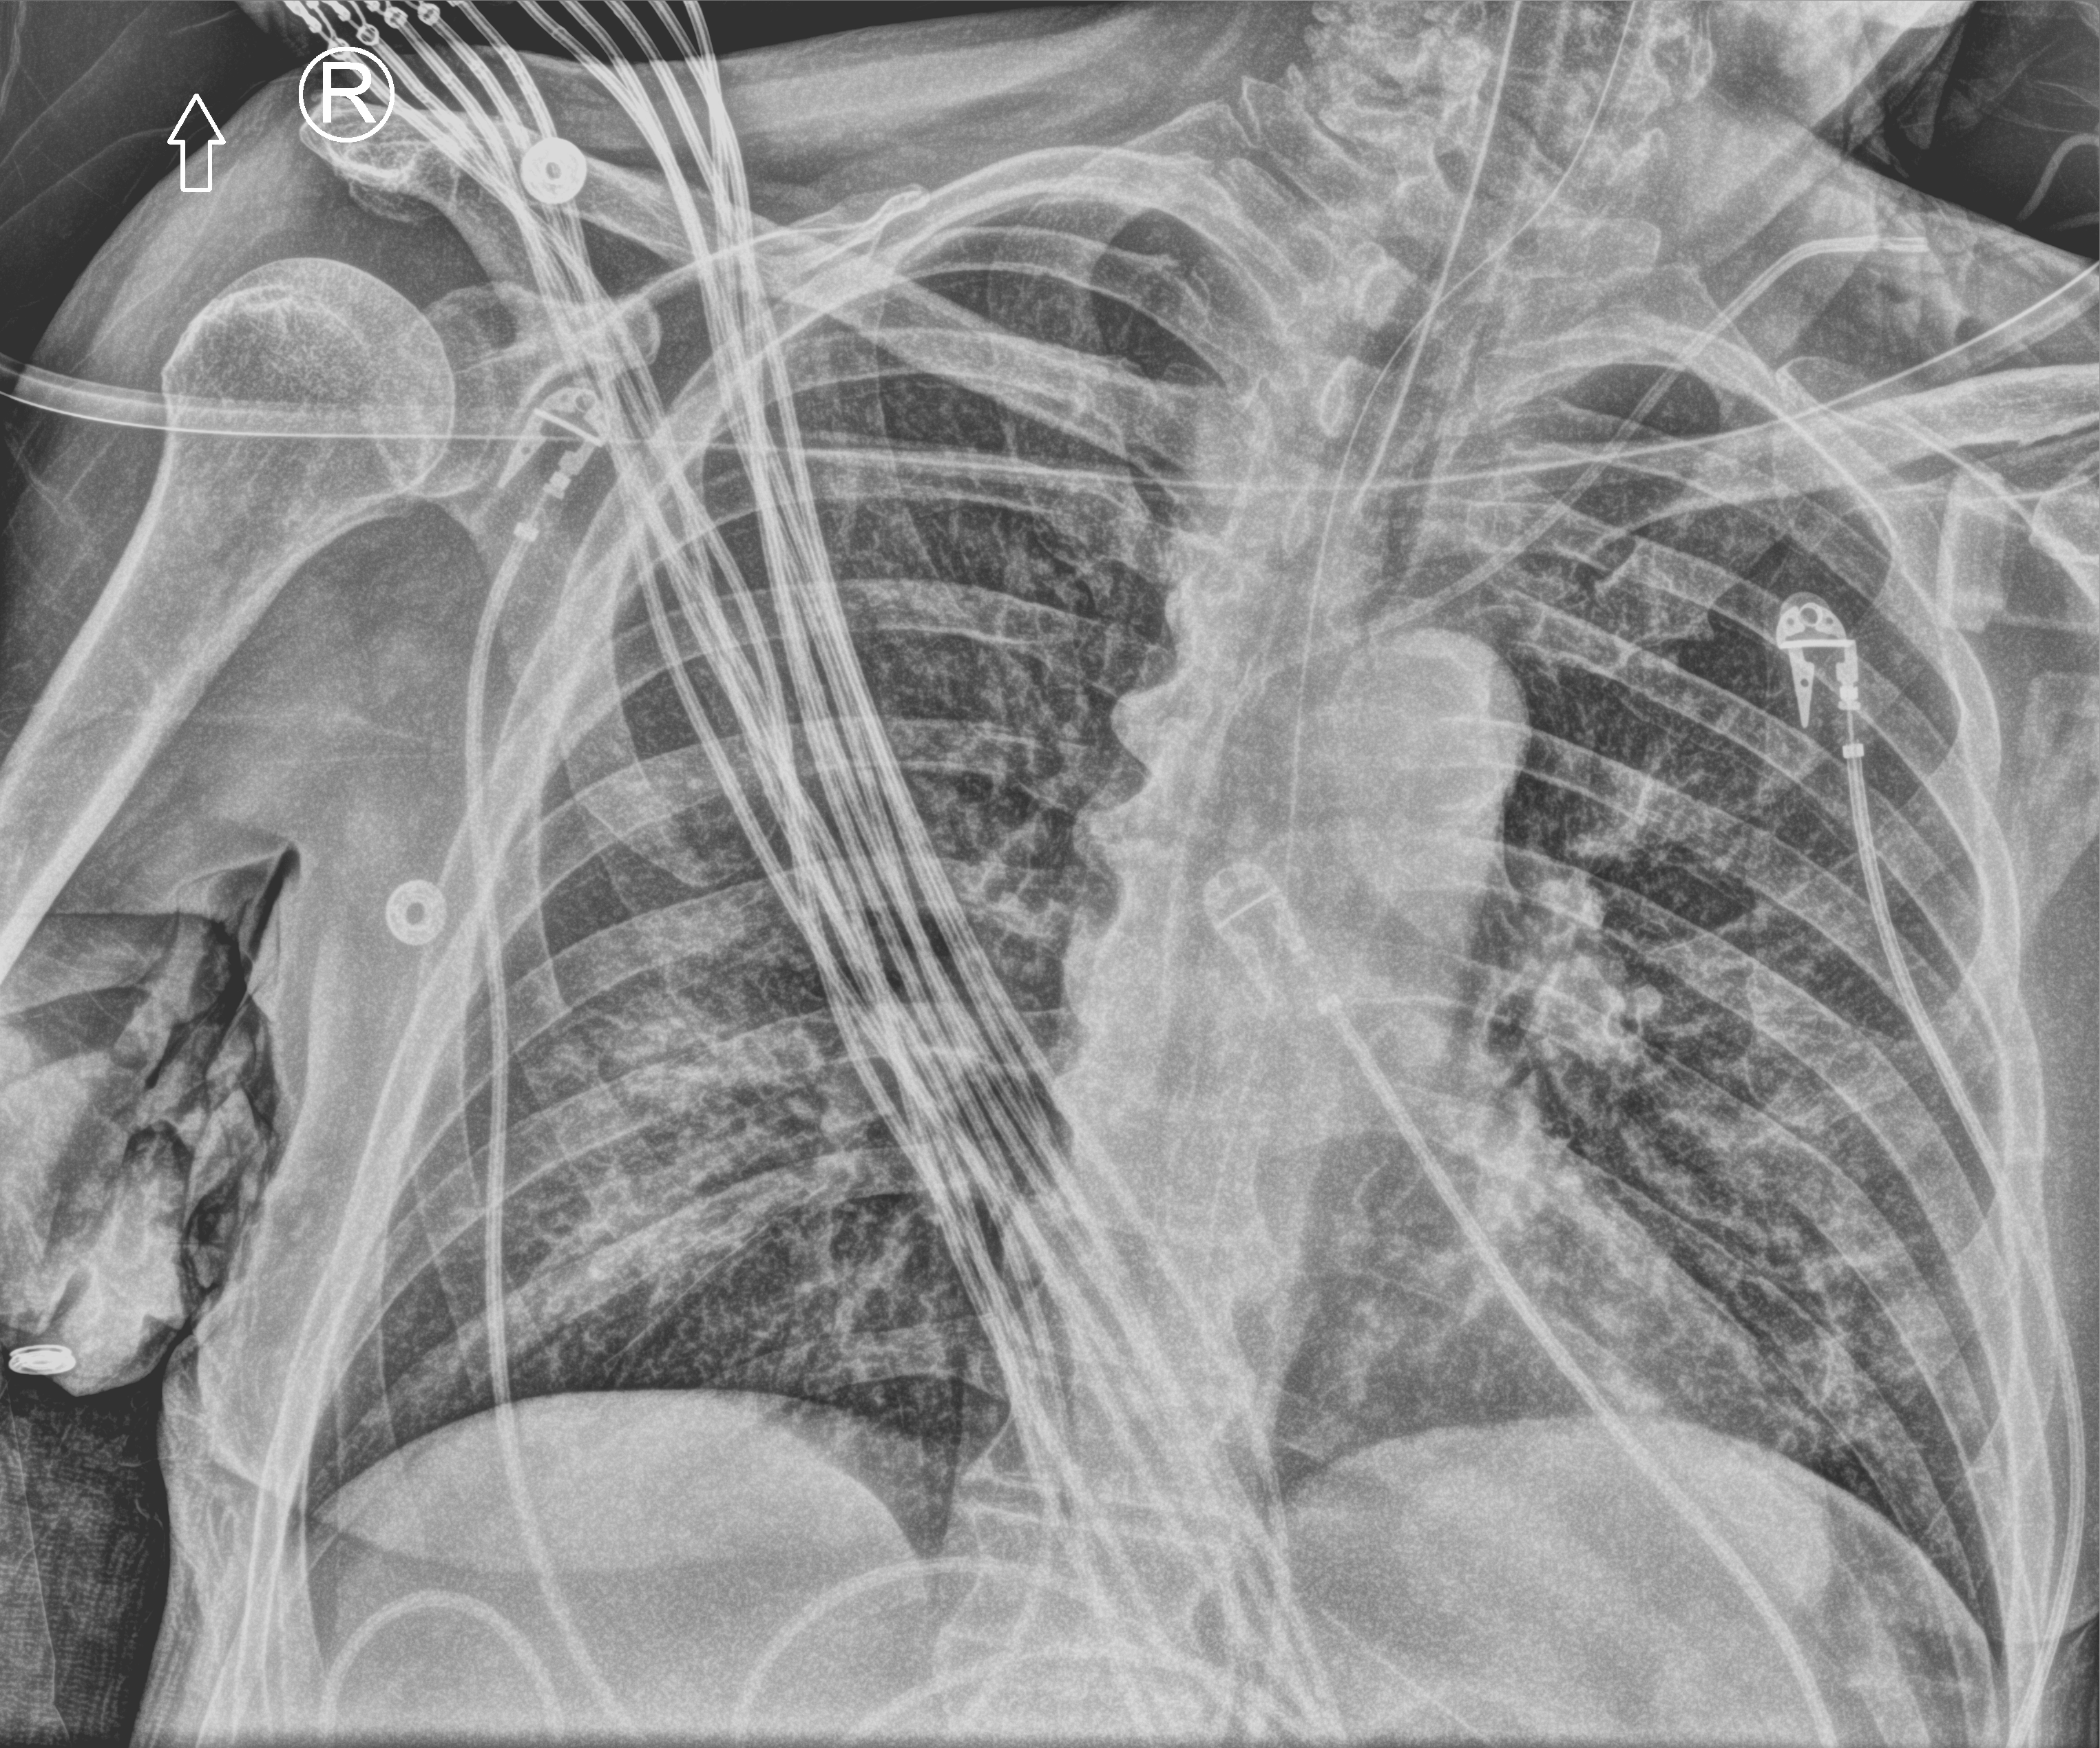
Portable chest radiograph, anteroposterior (AP) projection. Patient hospitalised with COVID-19; male, aged 60–74 years.
From the hospital-stay record, not from the radiograph (when in the stay this image was taken is not recorded):
- admitted to intensive care during this hospital stay: yes
- smoking status (admission record): never
- mechanically ventilated during this hospital stay: yes